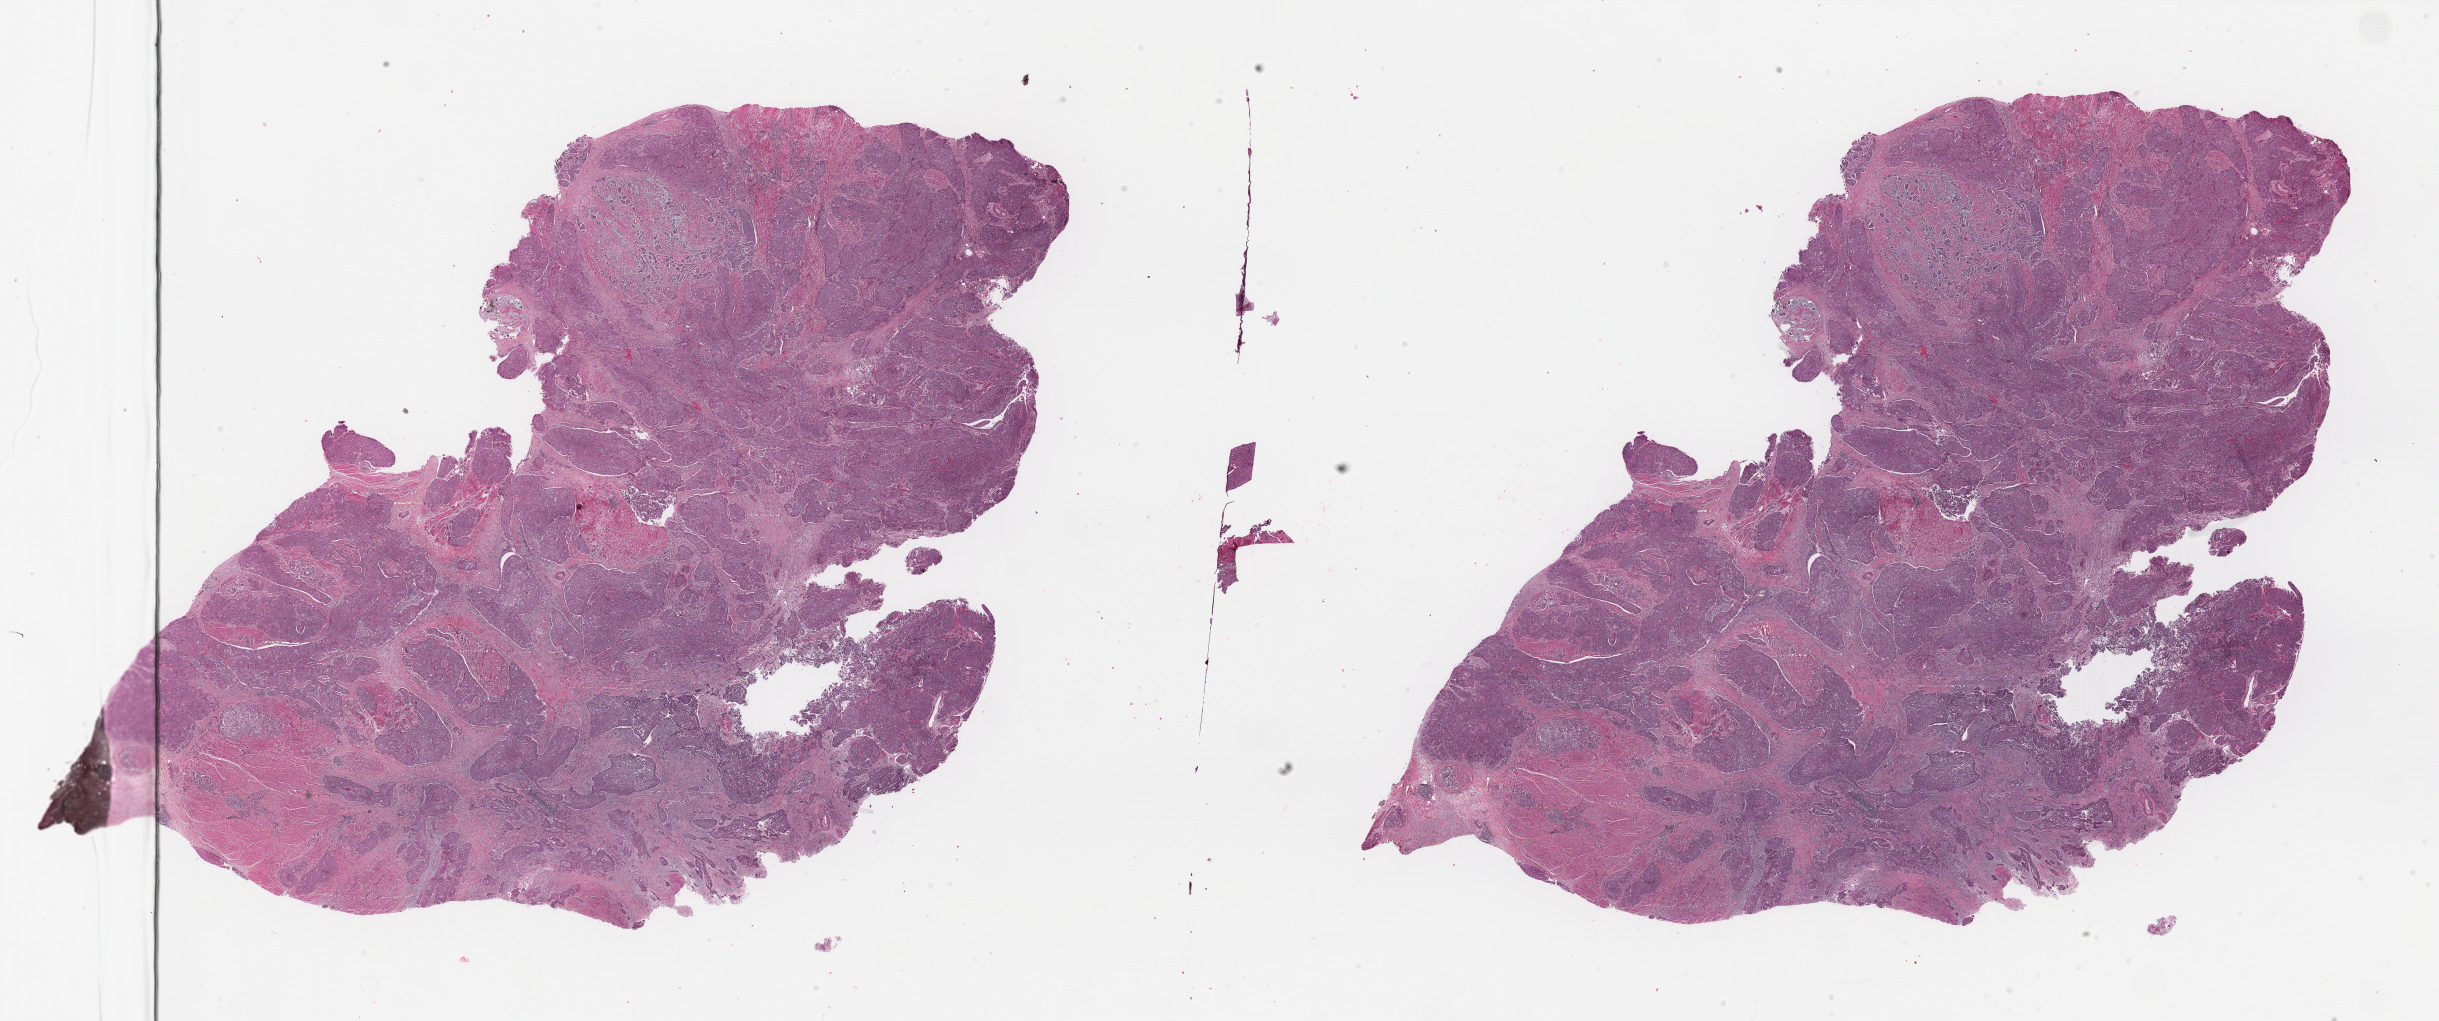
Hematoxylin and eosin (H&E) stained whole-slide image — low-resolution overview of the scanned area, about 38.6 x 16.2 mm (acquisition: 40x scan). Formalin-fixed paraffin-embedded (FFPE) diagnostic section. Sample: primary tumour, bladder. Male, age 76 years at initial diagnosis.
Pathologic diagnosis: Transitional cell carcinoma.